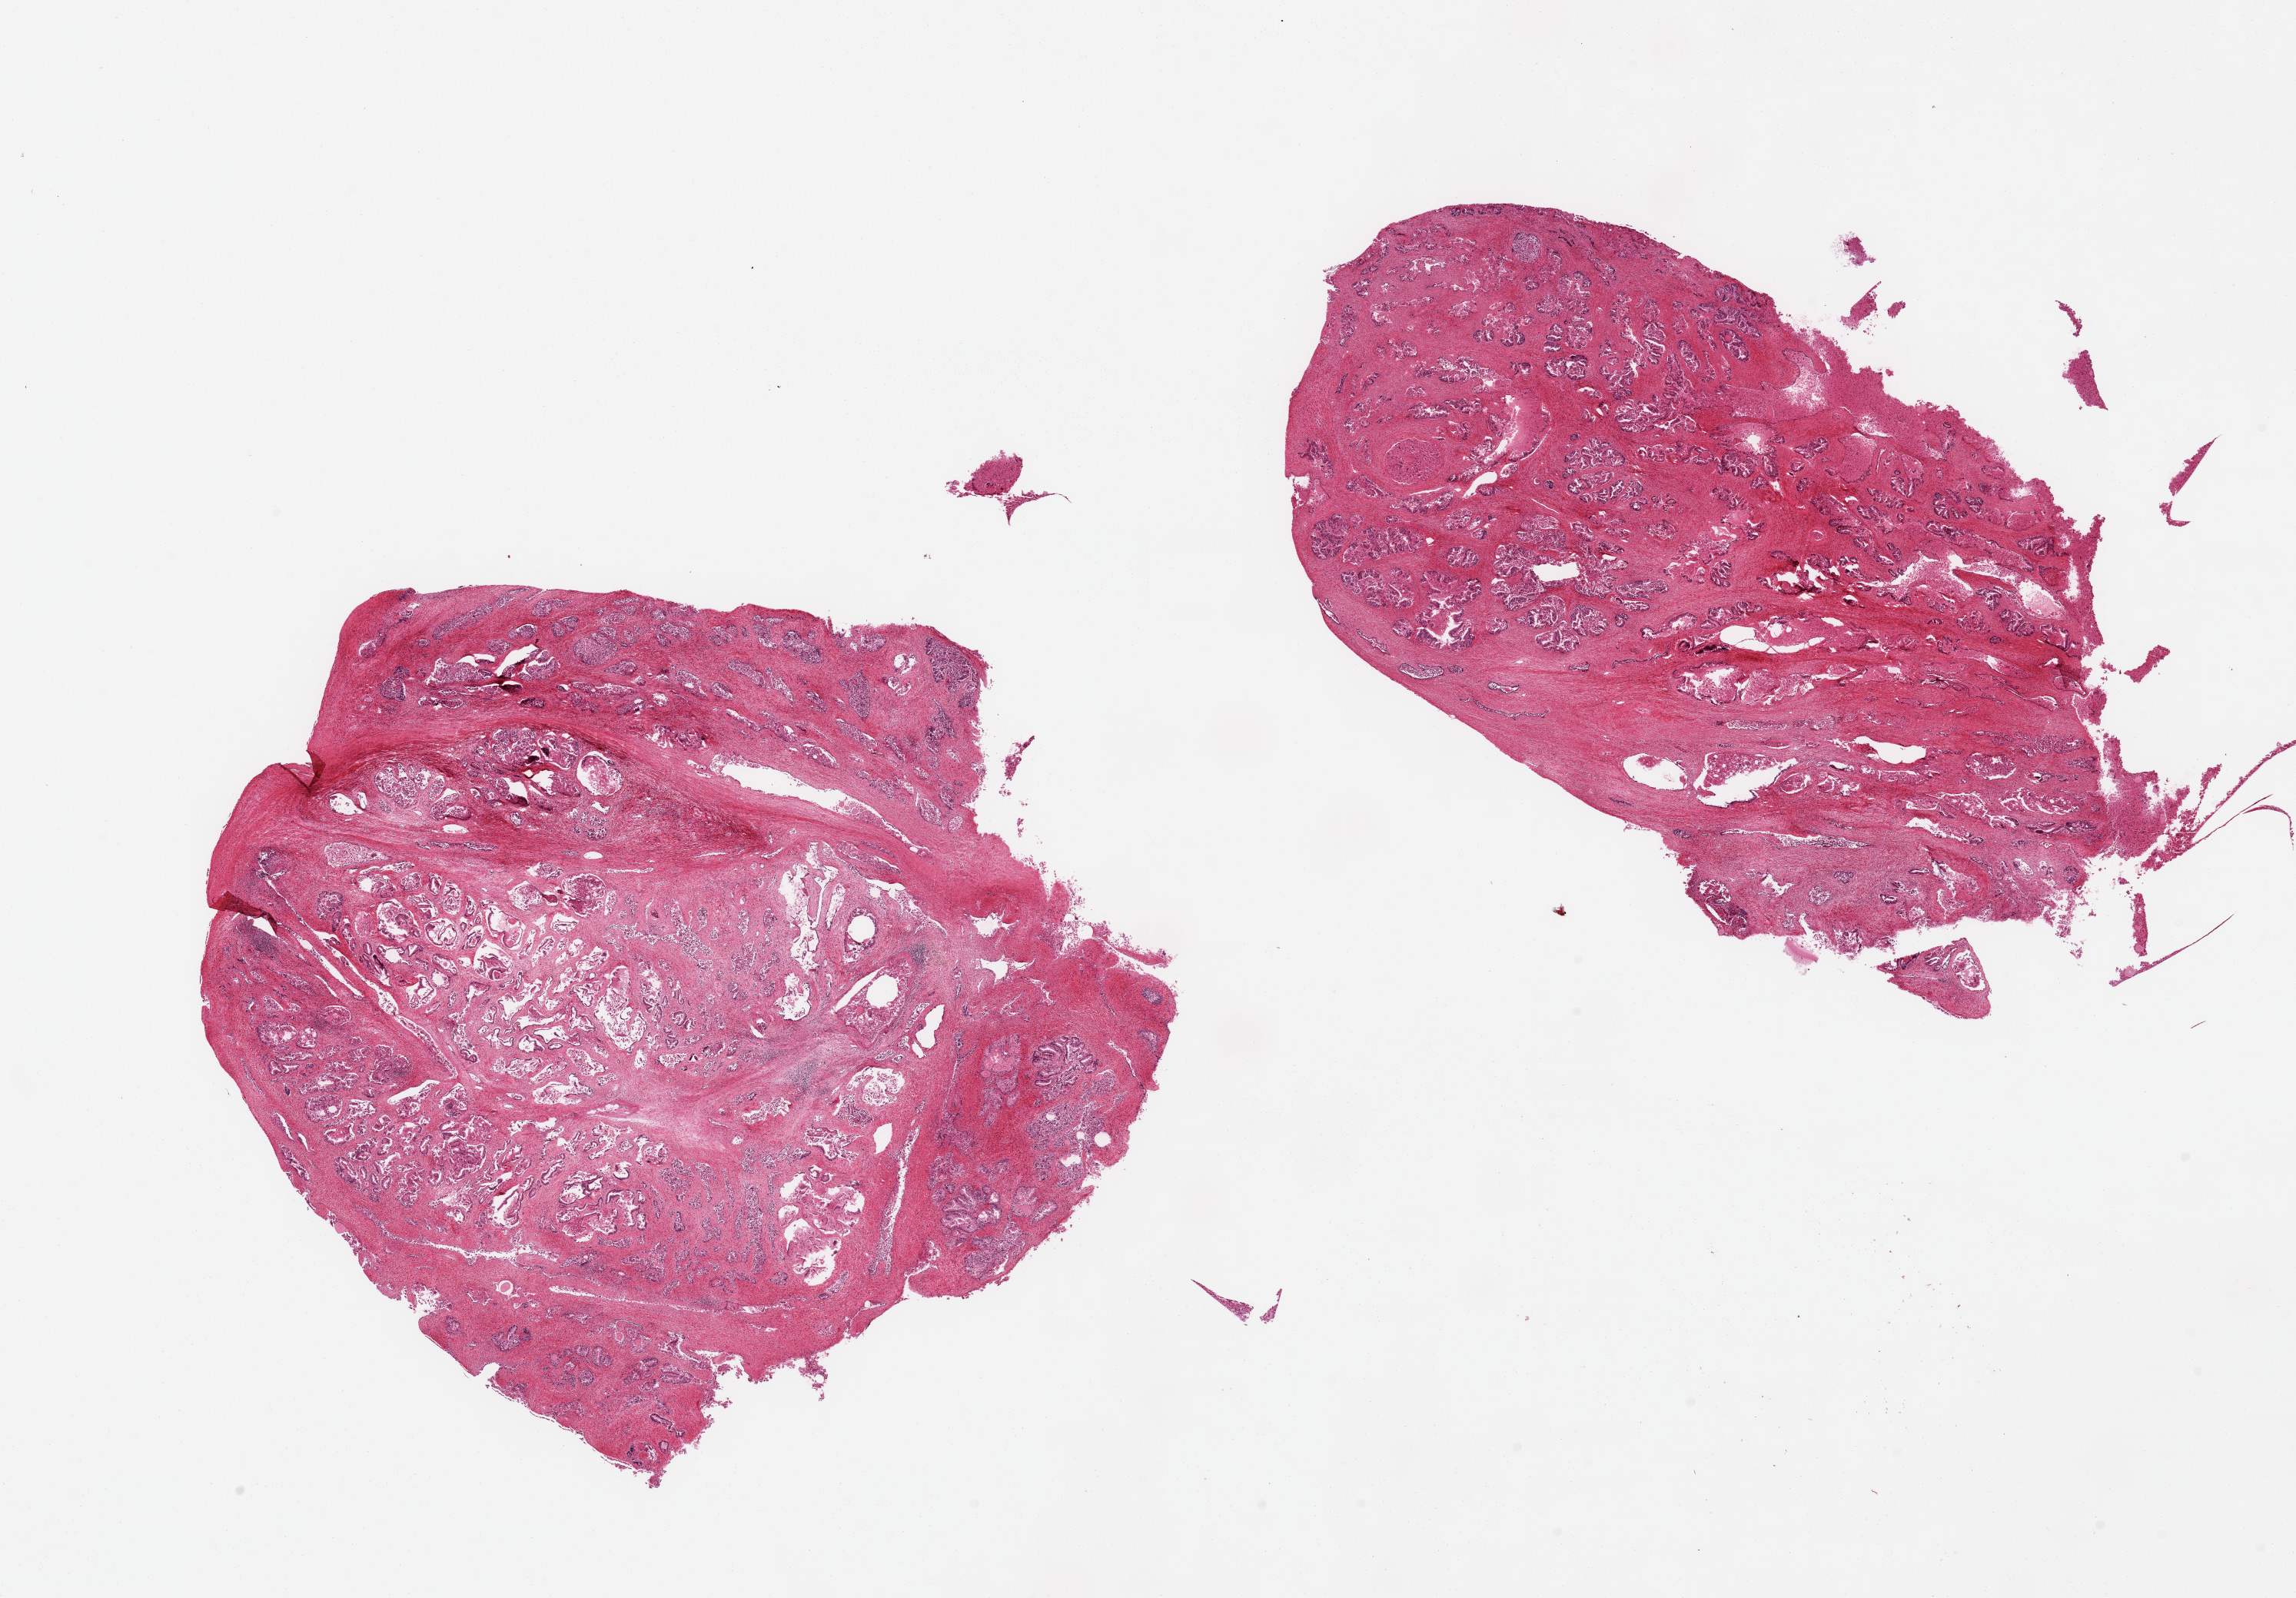
Hematoxylin and eosin (H&E) whole-slide image — shown as a low-resolution overview of the whole scanned area (about 23.6 x 16.4 mm, from a 20x scan). PAXgene-fixed paraffin-embedded (PFPE) section. Sampled site (target tissue): prostate. Donor tissue sample.
Review note (as recorded): 2 pieces, moderate-advanced glandular autolysis, hyperplastic glandular pattern.